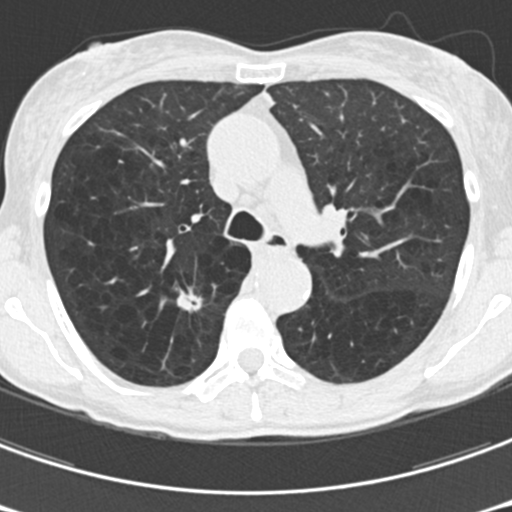
Low-dose screening chest CT, one axial slice. Slice 116 of 176 in the series (ordered by position). Reconstruction kernel B30f. Lung window (W 1500 / L -600 HU). 2 mm slice thickness. 512 × 512 image matrix.
Annotated regions visible in this slice (expert manual segmentation):
- lesion 1 (tumor, upper lobe of right lung): bounding box (x1, y1, x2, y2) in pixels: (177, 289, 202, 311)